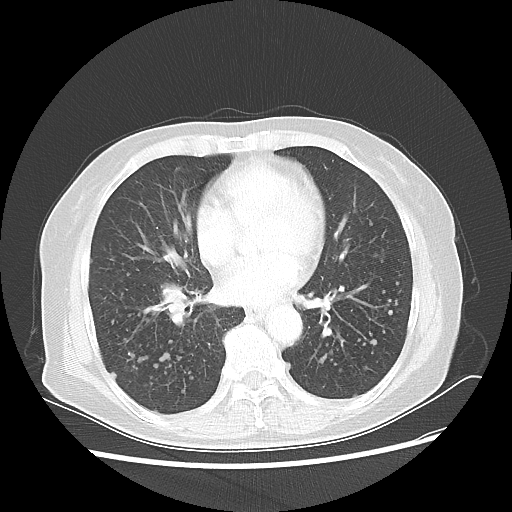
Chest CT, one axial slice. Position 24 of 56 along the scan axis. Reconstruction kernel LUNG. 80 kVp. Lung window (W 1500 / L -600 HU). 5 mm slice thickness. 512 × 512 image matrix. Patient: female, 68 years. Case-level facts recorded for this patient, not image findings: clinical TNM (as recorded): T1c N3 M0.
Outlined on this slice (bounding box drawn by a radiologist):
- lung tumour (recorded histology: squamous cell carcinoma): bounding box <155,280,189,306> (left, top, right, bottom; pixels)